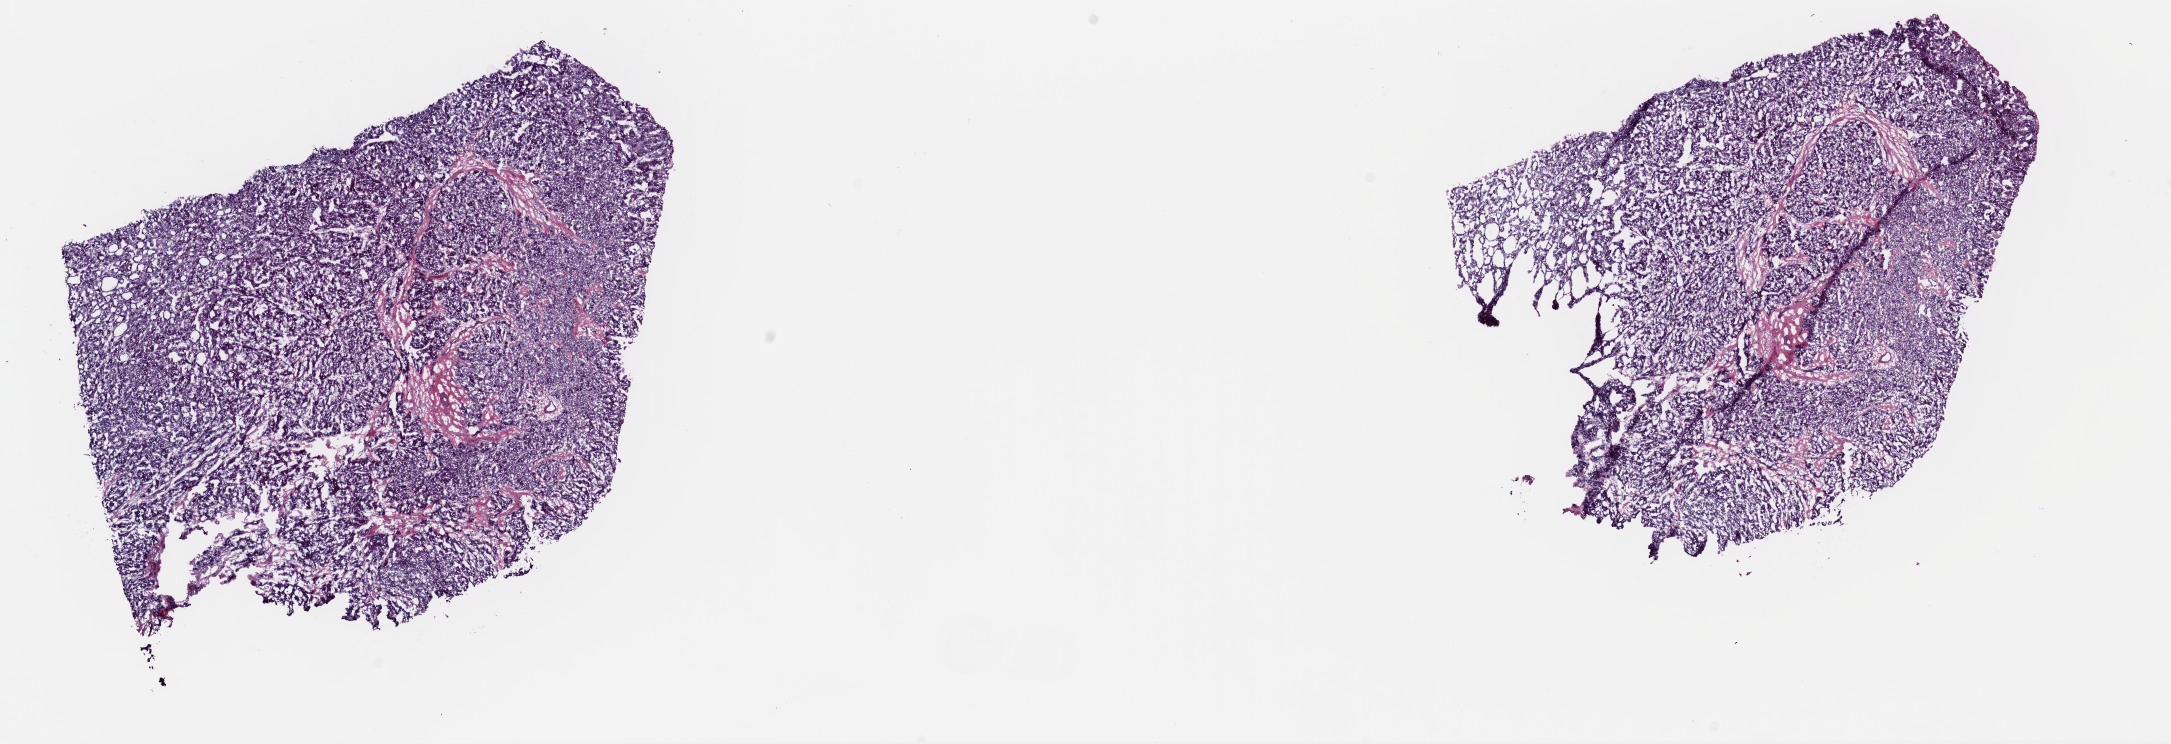
H&E-stained whole-slide image, low-resolution overview of the scanned area, about 17.2 x 5.9 mm (slide scanned at 40x). Frozen section. Primary tumour sample from the liver. Male, age 54 years at initial diagnosis. Histologic grade: G2 (moderately differentiated). Pathologist review of this section (percent, as recorded): tumour cells 90%, tumour nuclei 90%, normal cells 0%, stromal cells 10%, necrosis 0%. Inflammatory infiltration, as recorded: lymphocyte infiltration 0%, monocyte infiltration 0%, neutrophil infiltration 0%.
Histologic diagnosis: Hepatocellular carcinoma, NOS. TNM: T1 NX MX. AJCC pathologic stage: I (6th edition).